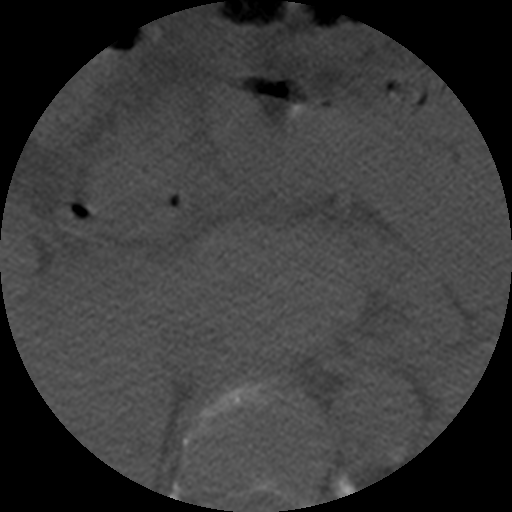
CT including the spine, one axial slice. Slice 254 of 508 in the series (ordered by position). Reconstruction kernel STANDARD. 120 kVp. Bone window (W 1800 / L 400 HU). 512 × 512 image matrix. Patient age 57 years. From the clinical record (not read from this slice): primary cancer: prostate.
Outlined on this slice (semi-automatically segmented with operator editing):
- T10 vertebra: bounding box (x1, y1, x2, y2) in pixels: (250, 477, 294, 498)
- T11 vertebra: (184, 381, 296, 464)